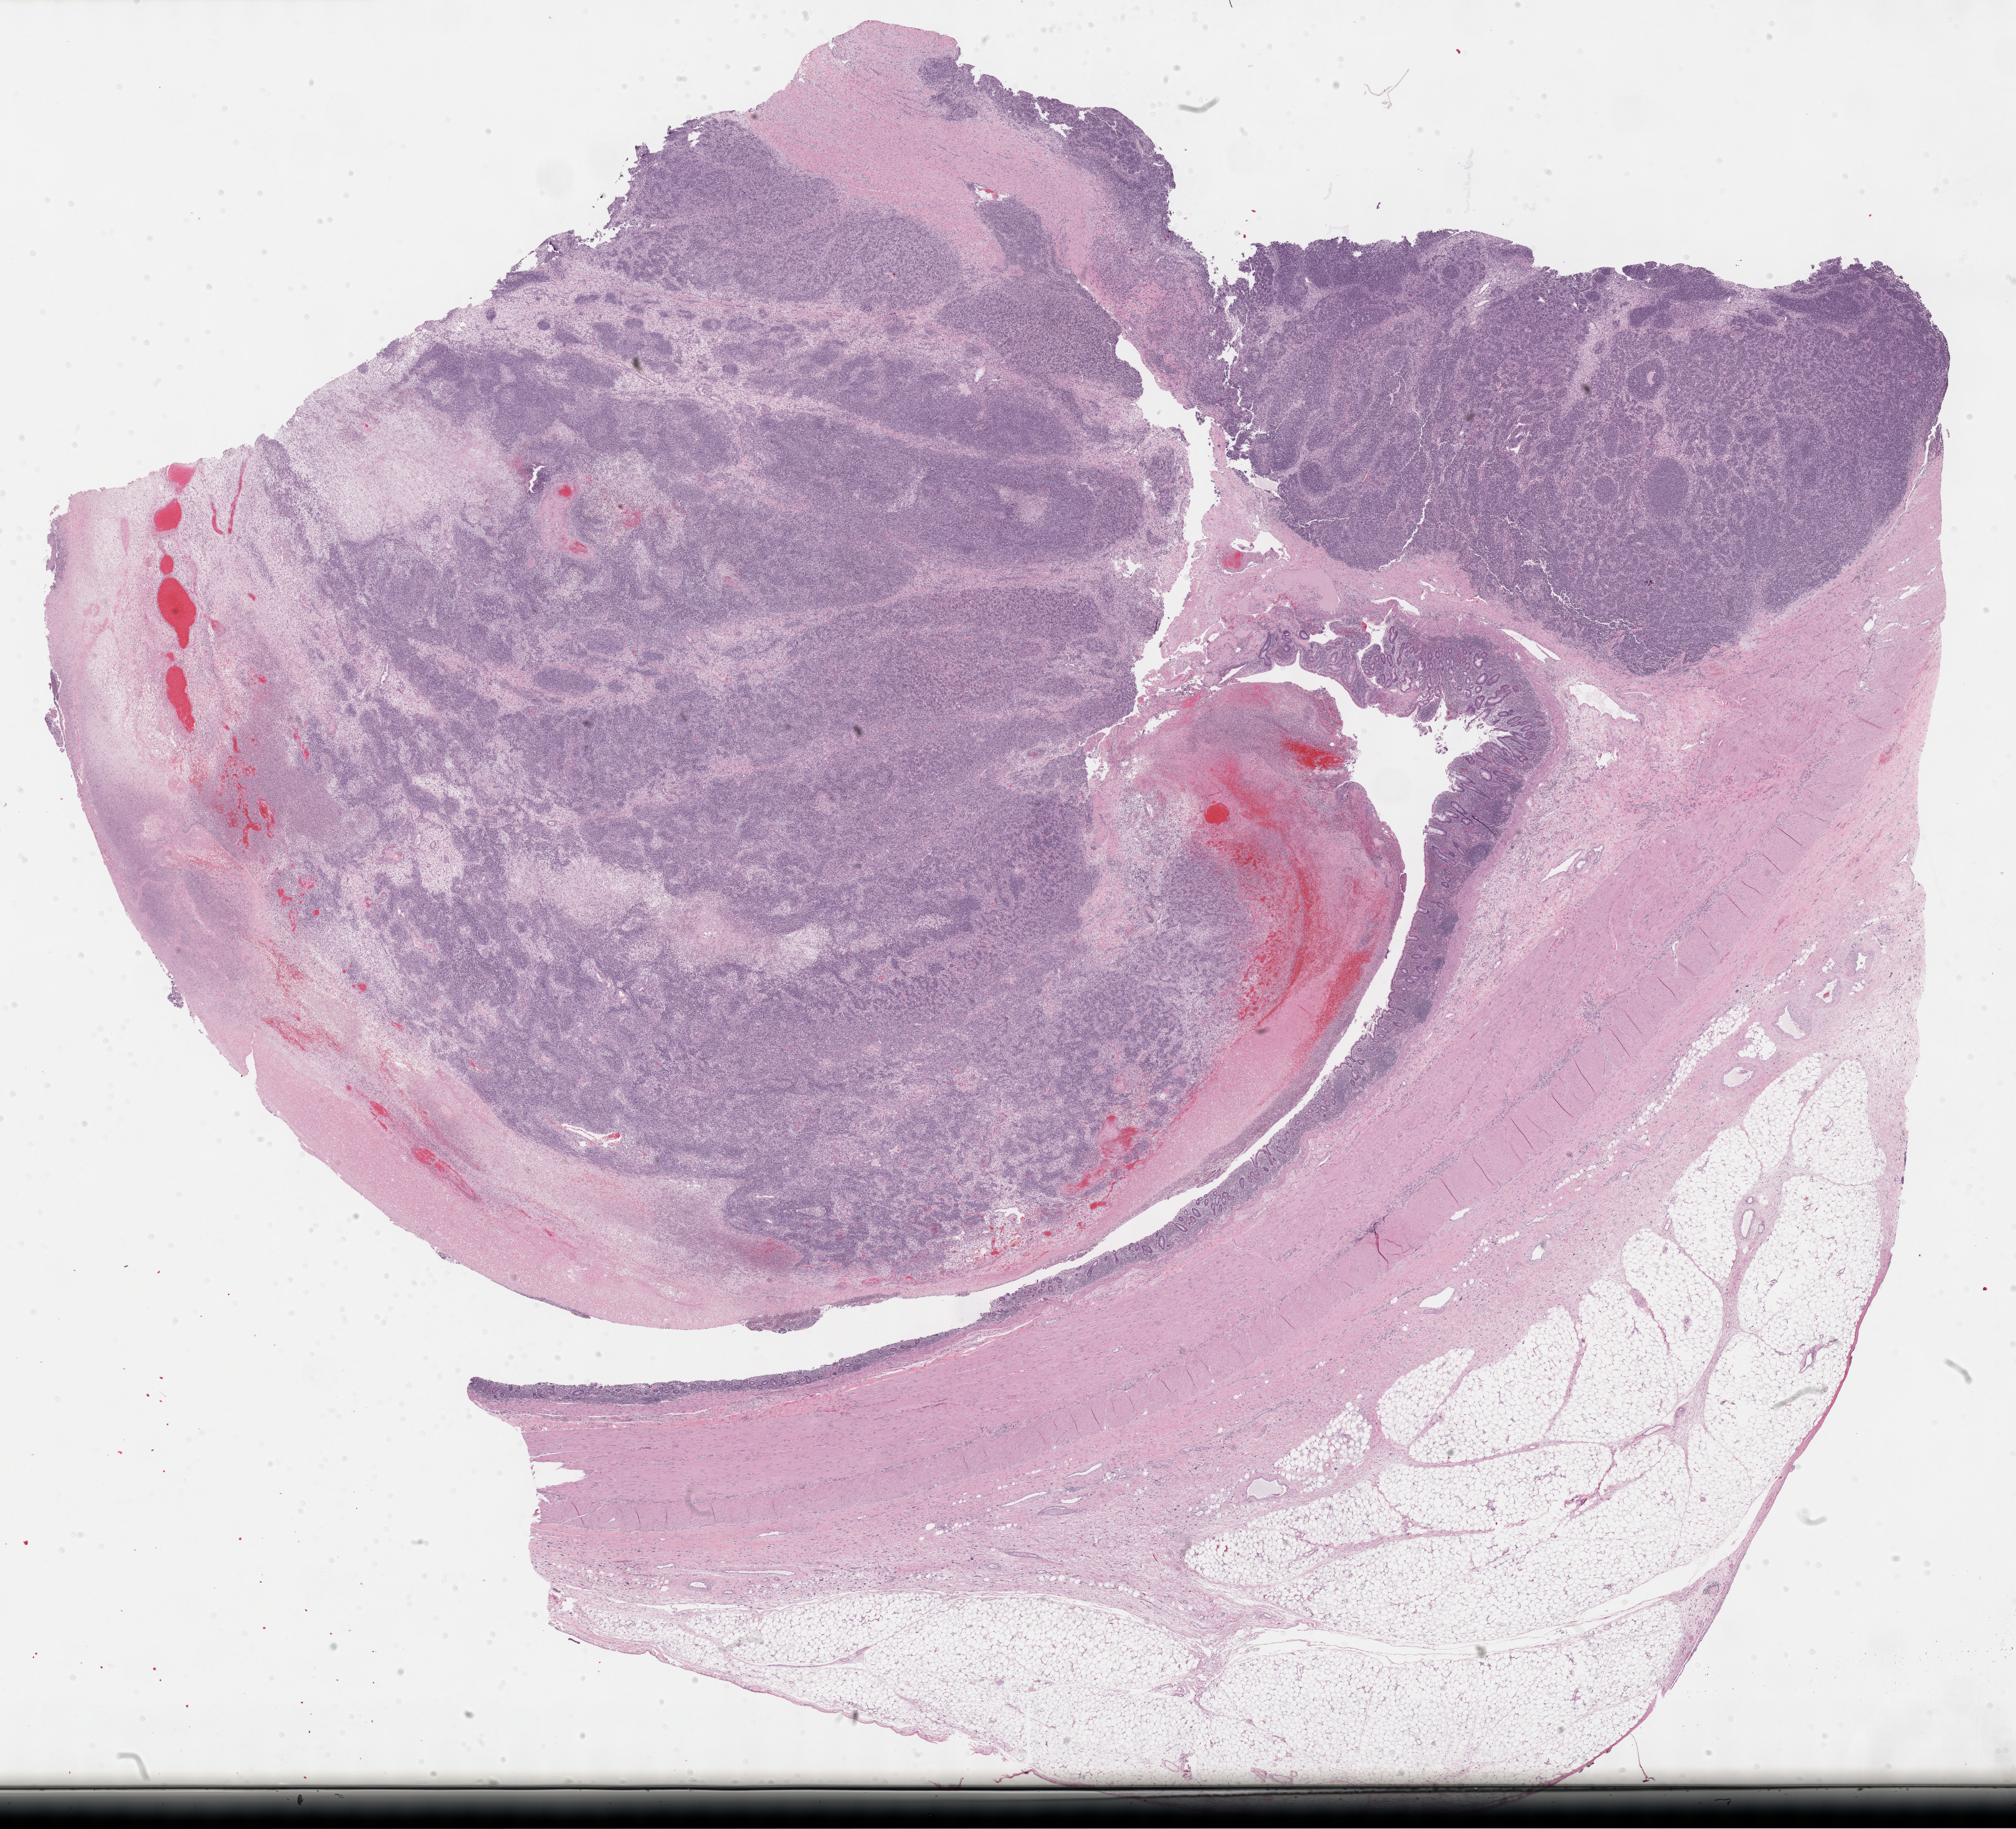
Hematoxylin and eosin (H&E) stained whole-slide image — a low-resolution overview of the entire scanned area, about 26.2 x 23.7 mm (from a 40x scan). Formalin-fixed paraffin-embedded (FFPE) diagnostic section. Retroperitoneum and peritoneum, primary tumour sample. Patient: female, age at initial diagnosis 80 years.
• pathologic diagnosis: Dedifferentiated liposarcoma (retroperitoneum)